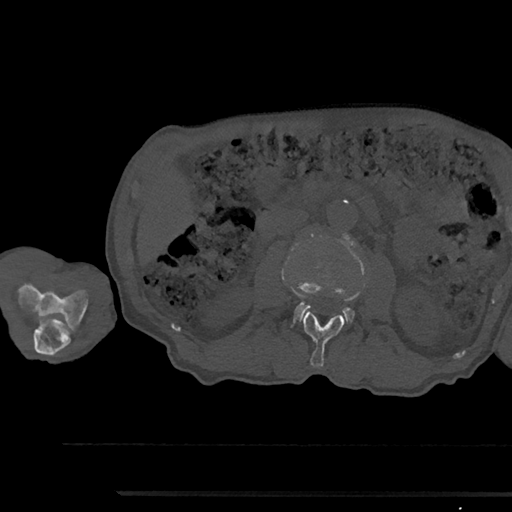
CT including the spine, one axial slice; slice 531 of 797 in the series (ordered by position); reconstruction kernel Br40s/3; bone window (W 1800 / L 400 HU); 0.5 mm slice thickness; 512 × 512 image matrix. Male patient, age 79 years. From the clinical record (not read from this slice): primary cancer: prostate.
Outlined on this slice (semi-automatically segmented with operator editing):
- L2 vertebra: bounding box <302,311,345,367> (left, top, right, bottom; pixels)
- L3 vertebra: <294,234,366,322>